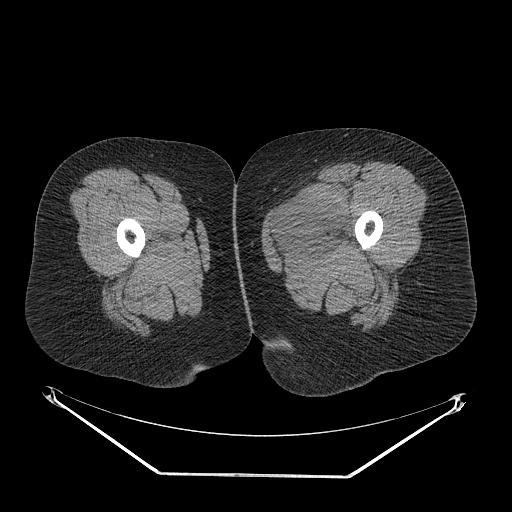
CT of an extremity soft-tissue mass (from a PET/CT study), one axial slice. Slice 19 of 267 in the series (ordered by position). 140 kVp. Soft-tissue window (W 400 / L 40 HU). 3.75 mm slice thickness. 512 × 512 image matrix, field of view 500 × 500 mm. Female patient. From the clinical record (not read from this slice): histological type: myxofibrosarcoma; grade: intermediate; site of the primary tumour: left thigh.
Annotated regions visible in this slice (expert contour drawn on MRI and transferred to this co-registered scan by the dataset authors):
- gross tumour volume including surrounding oedema: bounding box [x1, y1, x2, y2] px = [272, 190, 350, 255]
- gross tumour volume (mass): [274, 192, 348, 255]